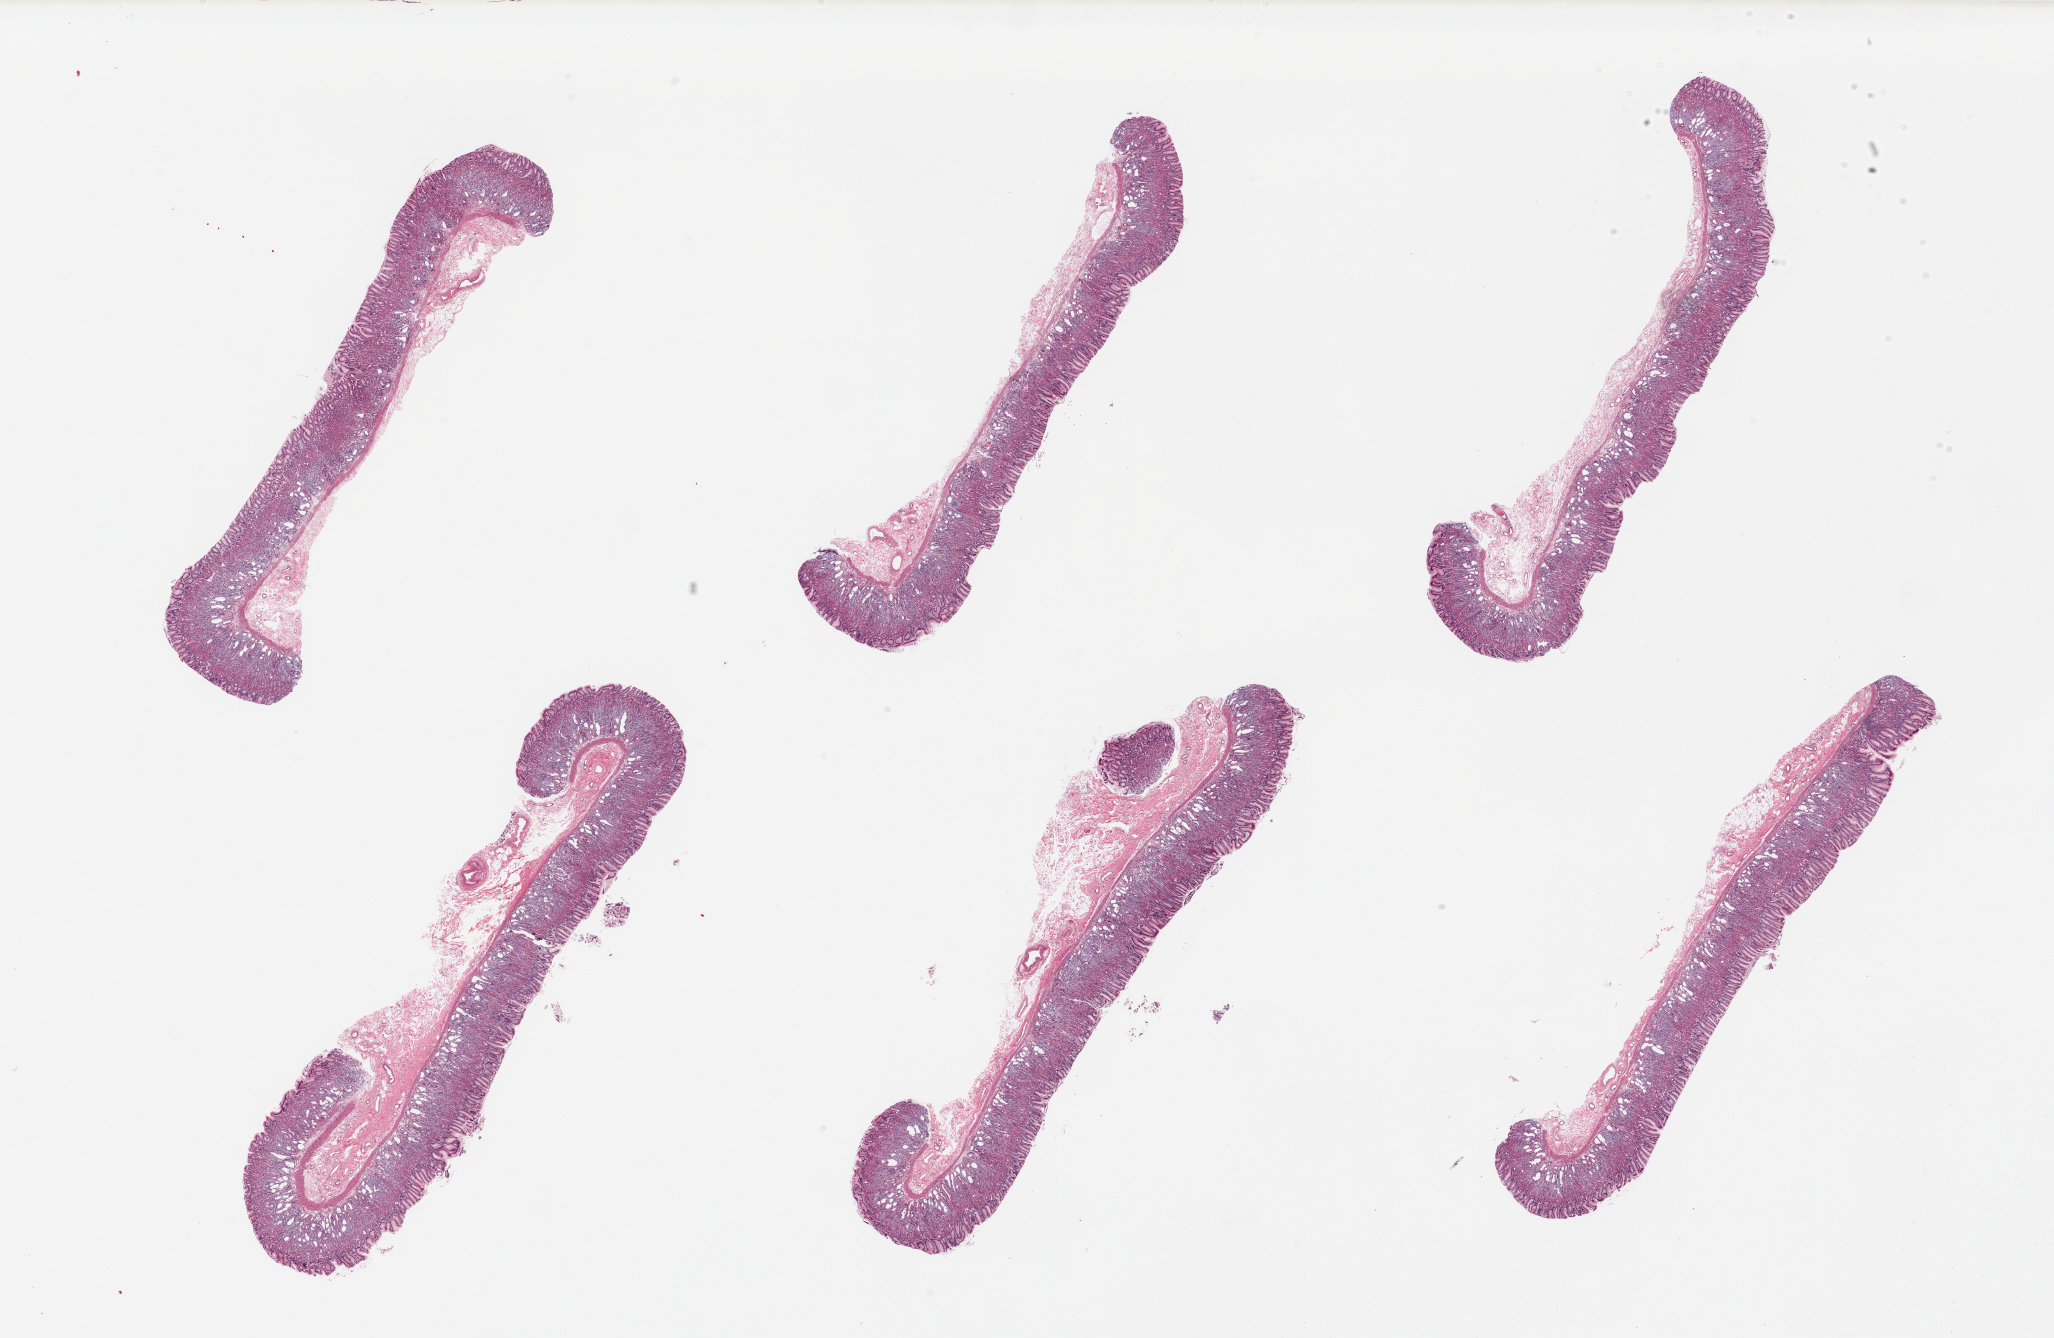
H&E whole-slide image, brightfield, whole scanned area (about 32.5 x 21.2 mm, from a 20x scan) shown as a low-resolution overview; PAXgene-fixed paraffin-embedded (PFPE) section; target tissue: stomach; tissue donor sample. Female donor.
Pathologist's review note for this sample: 6 pieces, well trimmed.